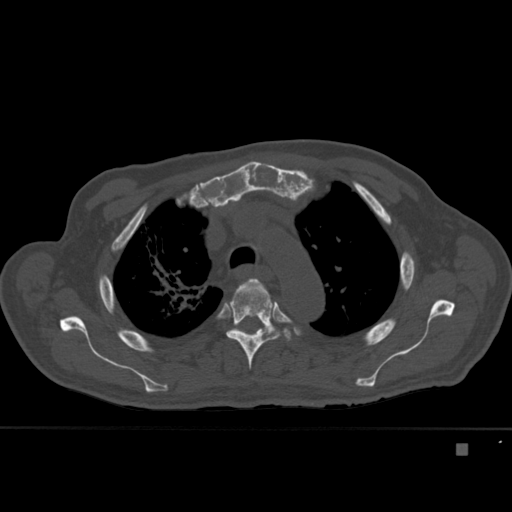
CT including the spine, one axial slice; position 321 of 451 along the scan axis; bone window (W 1800 / L 400 HU); 1.5 mm slice thickness; 512 × 512 image matrix, field of view 378 × 378 mm. Patient: male, 75 years. From the clinical record (not read from this slice): primary cancer: prostate.
Annotated regions visible in this slice (semi-automatic segmentation, software-assisted and operator-edited):
- T3 vertebra: bounding box <255,279,269,294> (left, top, right, bottom; pixels)
- T4 vertebra: <226,278,291,369>
- T5 vertebra: <235,325,267,331>